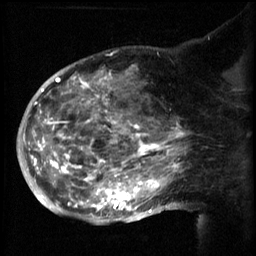
Breast MRI (dynamic contrast-enhanced), one sagittal slice. 3 images stored at this slice position (order not interpretable as contrast timing). 1.5 T. TE 4.2 ms, TR 8.2 ms. 256 × 256 image matrix. Female patient, age 50 years.
Annotated regions visible in this slice (semi-automatically segmented with operator editing):
- analysis volume of interest (the breast-tissue region the enhancement analysis was run in; not a lesion): bounding box (x1, y1, x2, y2) in pixels: (50, 64, 169, 217)
- tumour enhancement mask (voxels above the 70 % enhancement threshold inside the analysis volume of interest): (50, 68, 169, 215)